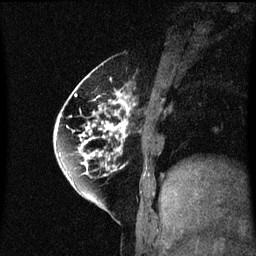
Breast MRI (dynamic contrast-enhanced), one sagittal slice. Slice 20 of 60 in the series (ordered by position). Dynamic contrast-enhanced series, image 2 of 3 at this slice position (ordered by acquisition). 1.5 T. TE 4.2 ms, TR 8.4 ms. 2 mm slice thickness. 256 × 256 image matrix, field of view 200 × 200 mm. Patient: female, 60 years.
Annotated regions visible in this slice (semi-automatic segmentation, software-assisted and operator-edited):
- analysis volume of interest (the breast-tissue region the enhancement analysis was run in; not a lesion): box from (x=64, y=70) to (x=133, y=195) px
- tumour enhancement mask (voxels above the 70 % enhancement threshold inside the analysis volume of interest): (x=64, y=70)–(x=131, y=185)